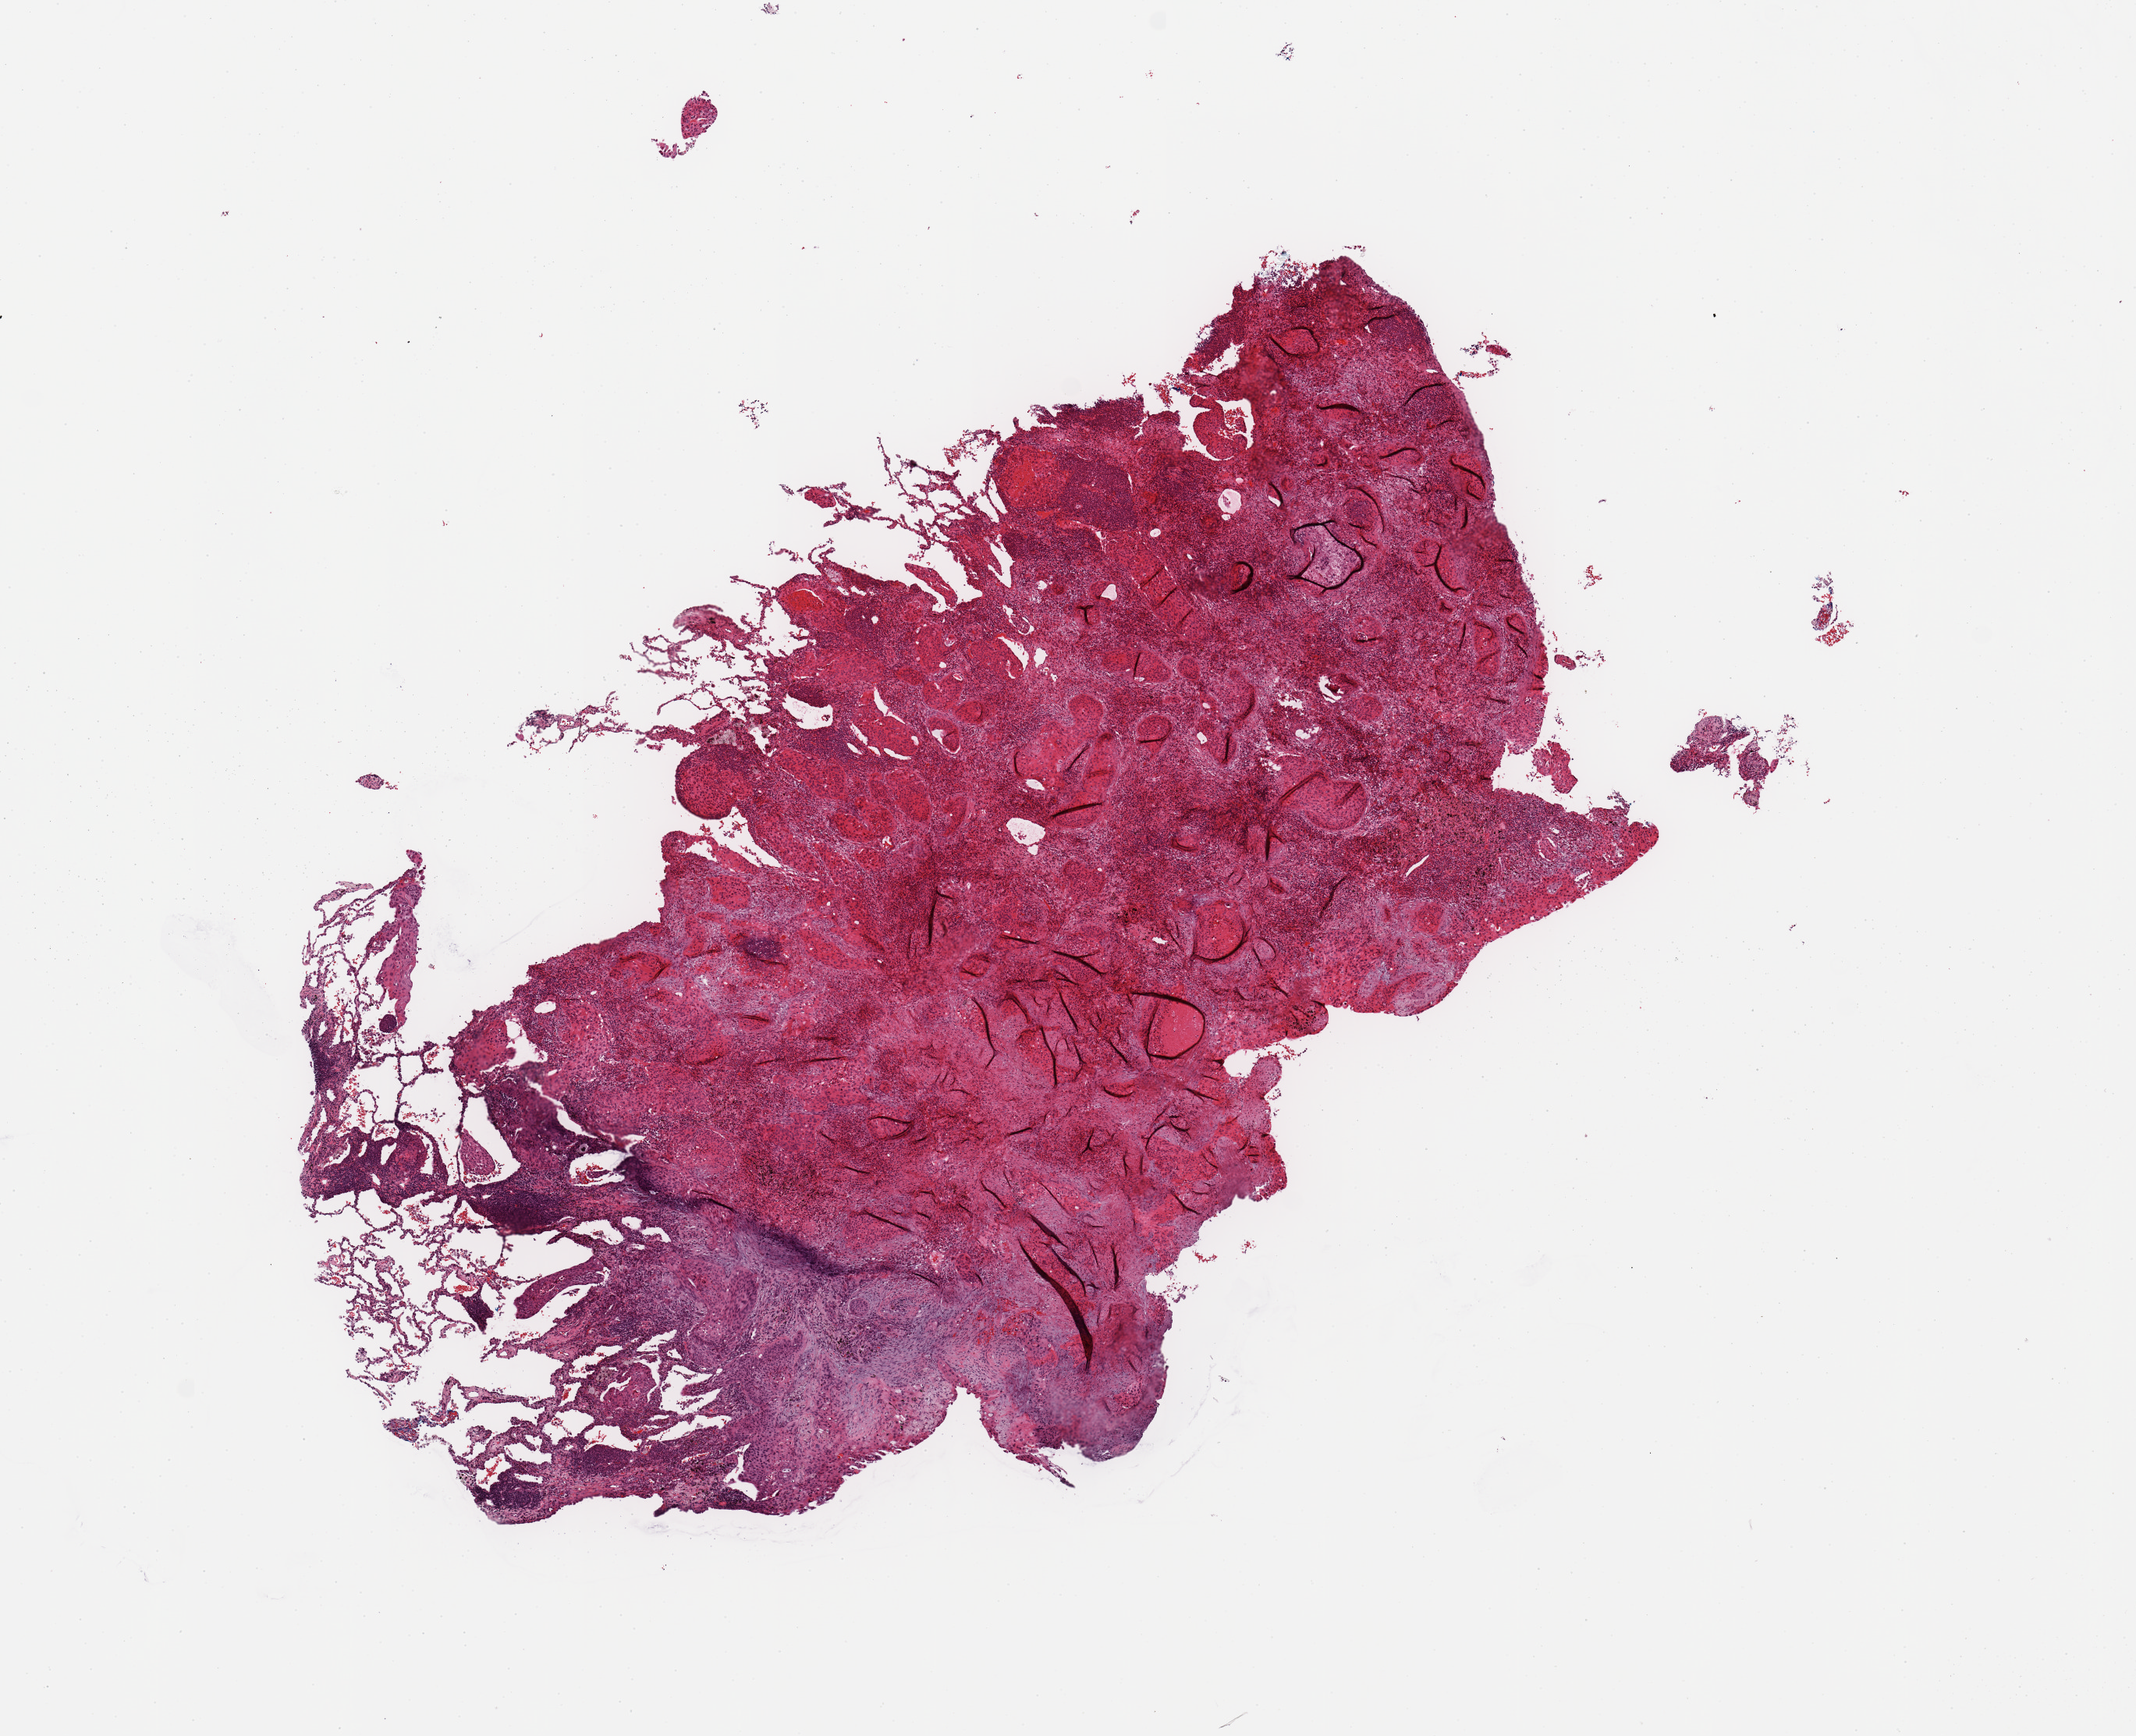
Hematoxylin and eosin (H&E) stained whole-slide image — whole scanned area (about 10.8 x 8.8 mm, slide scanned at 20x) shown as a low-resolution overview; lung, tumour tissue. 74-year-old male patient. Histologic grade: G2 (moderately differentiated).
• primary tumour site (as recorded): left upper lobe
• AJCC pathologic stage: IB
• histologic diagnosis: Squamous cell carcinoma, NOS